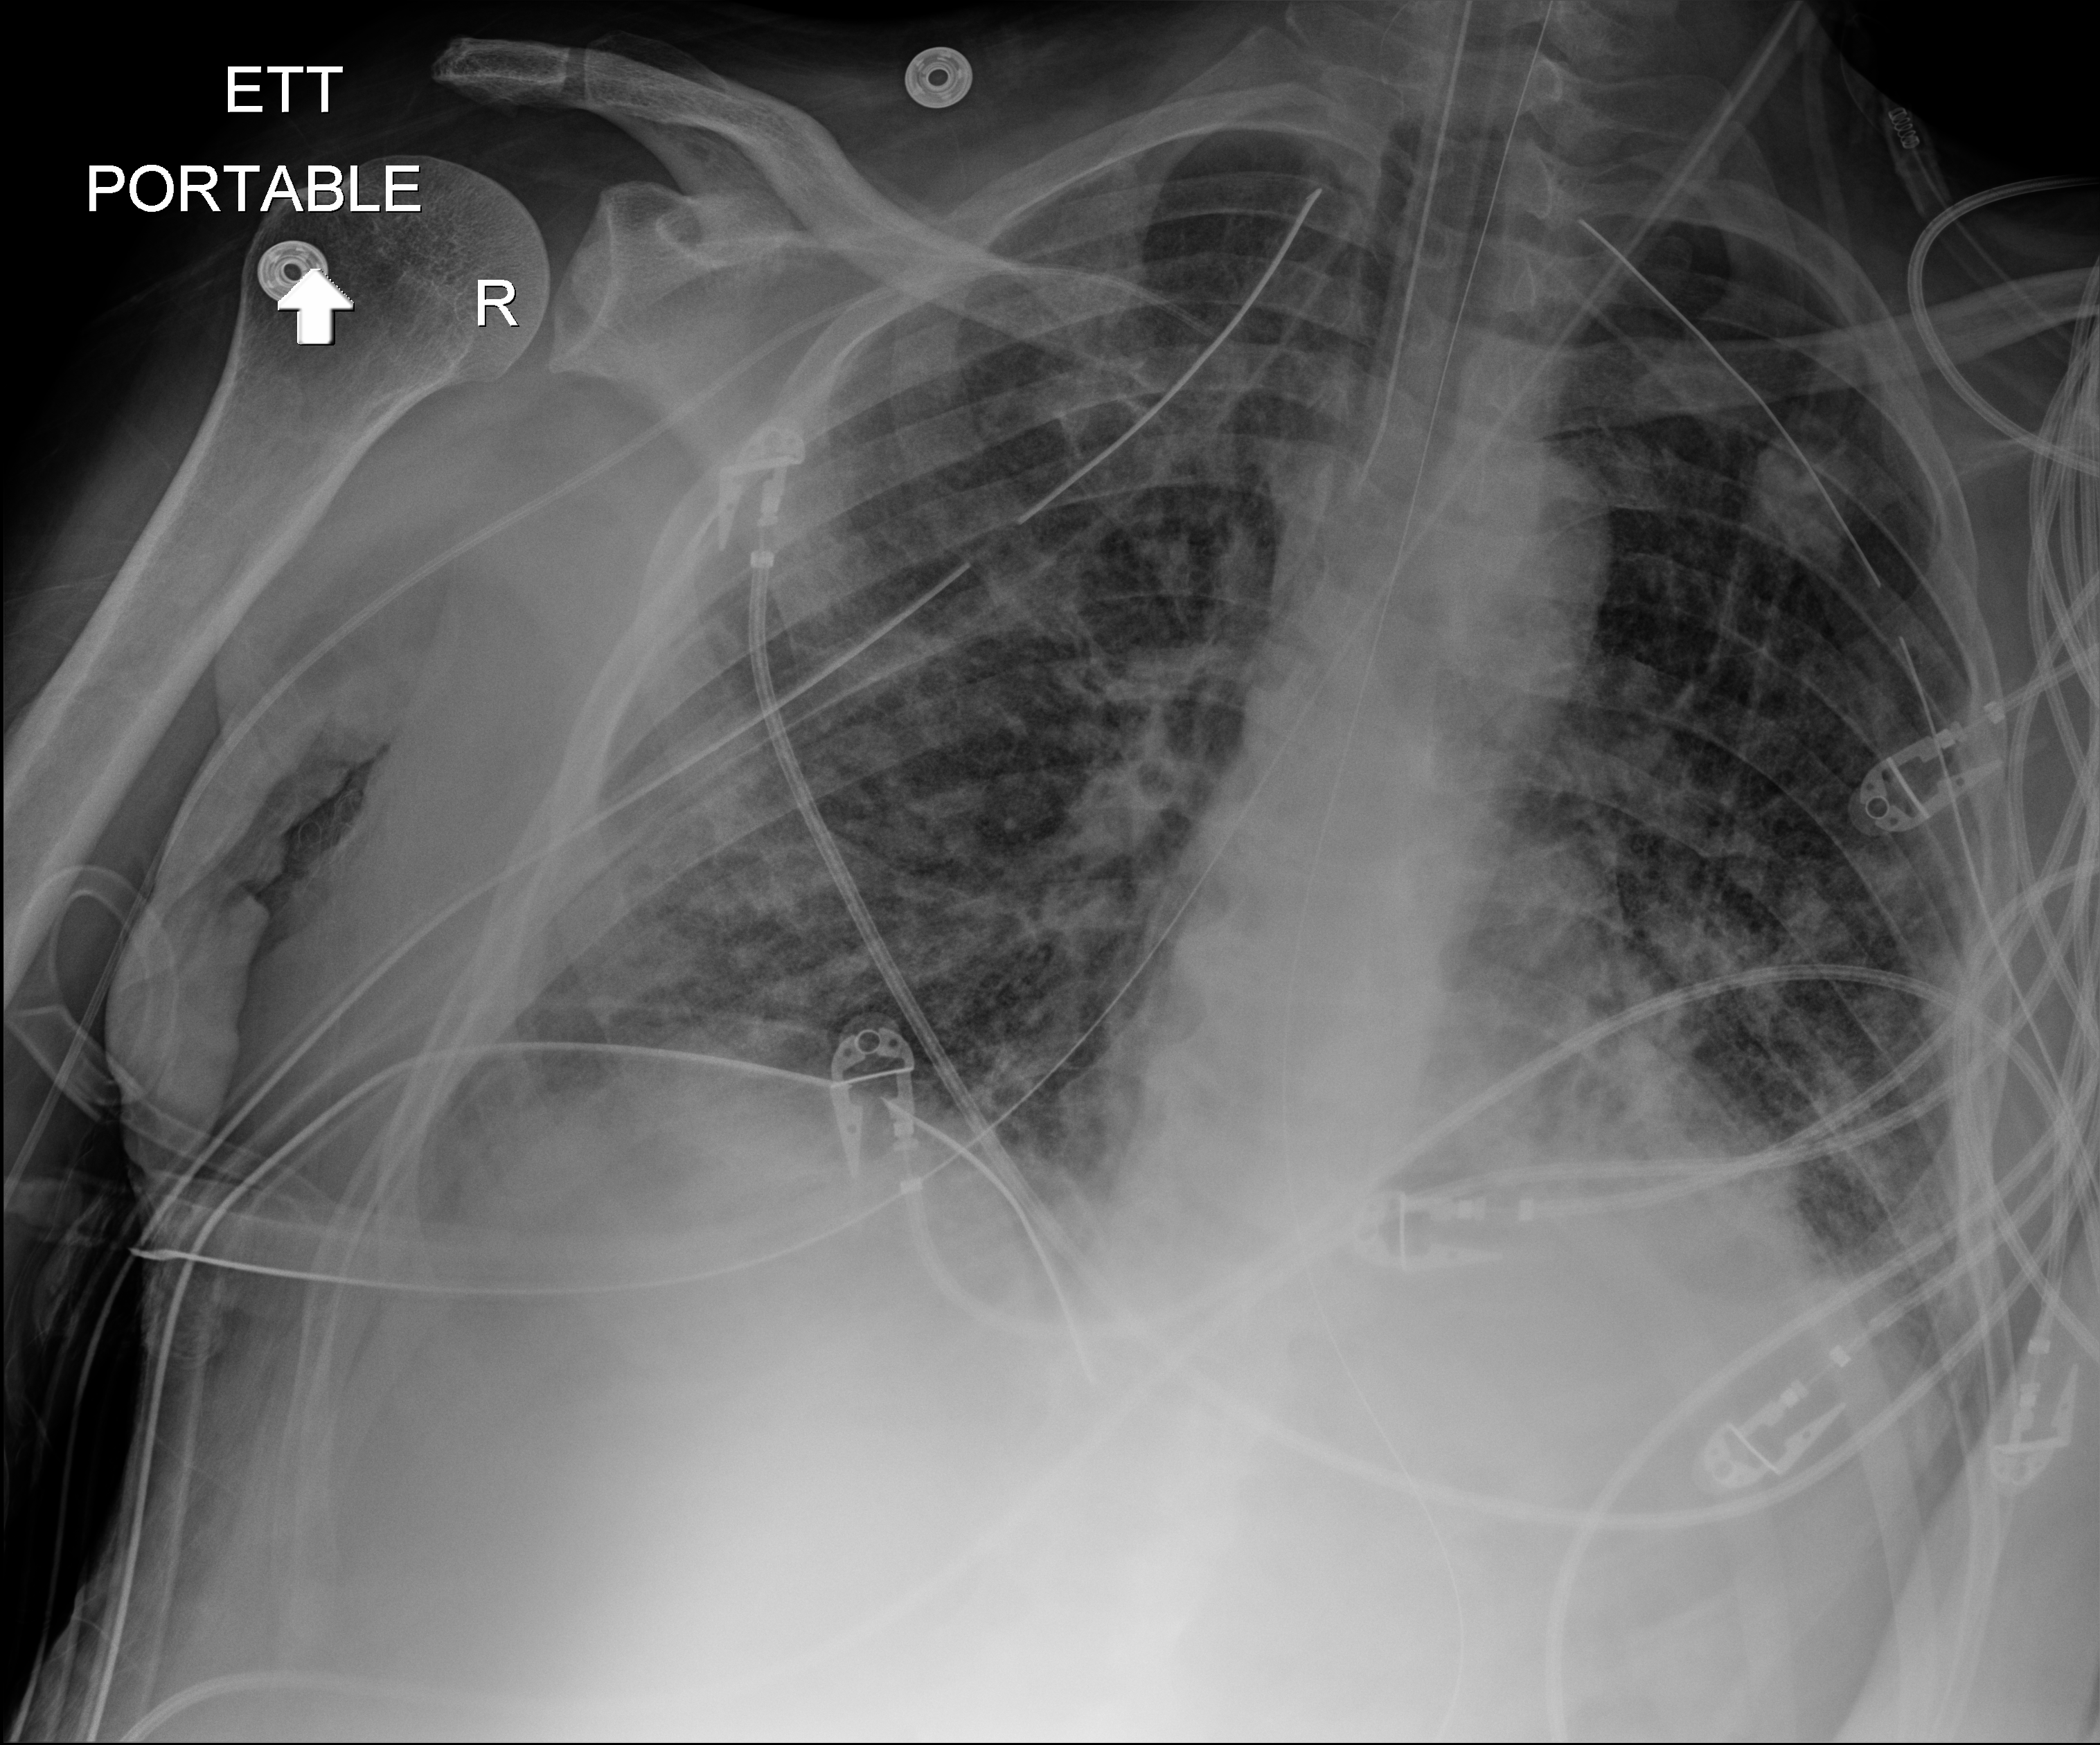
Portable chest radiograph, anteroposterior (AP) projection. Patient hospitalised with COVID-19; male, aged 18–59 years.
Admission-level facts for this patient (not findings on this image; timing relative to this image not recorded): COPD (admission record): no.